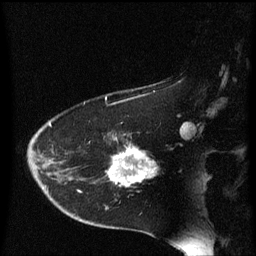
Breast MRI (dynamic contrast-enhanced), one sagittal slice; slice 42 of 60 in the series (ordered by position); dynamic contrast-enhanced series, image 2 of 3 at this slice position (ordered by acquisition); 1.5 T; TE 4.2 ms, TR 8.4 ms; 2 mm slice thickness; 256 × 256 image matrix, field of view 200 × 200 mm. Female patient, age 54 years. Case-level facts recorded for this patient, not image findings: setting: breast cancer imaged before/during neoadjuvant chemotherapy; receptor status: HR-positive, HER2-negative.
Annotated regions visible in this slice (semi-automatic segmentation, software-assisted and operator-edited):
- analysis volume of interest (the breast-tissue region the enhancement analysis was run in; not a lesion): box from (x=102, y=132) to (x=156, y=187) px
- tumour enhancement mask (voxels above the 70 % enhancement threshold inside the analysis volume of interest): (x=111, y=148)–(x=156, y=187)